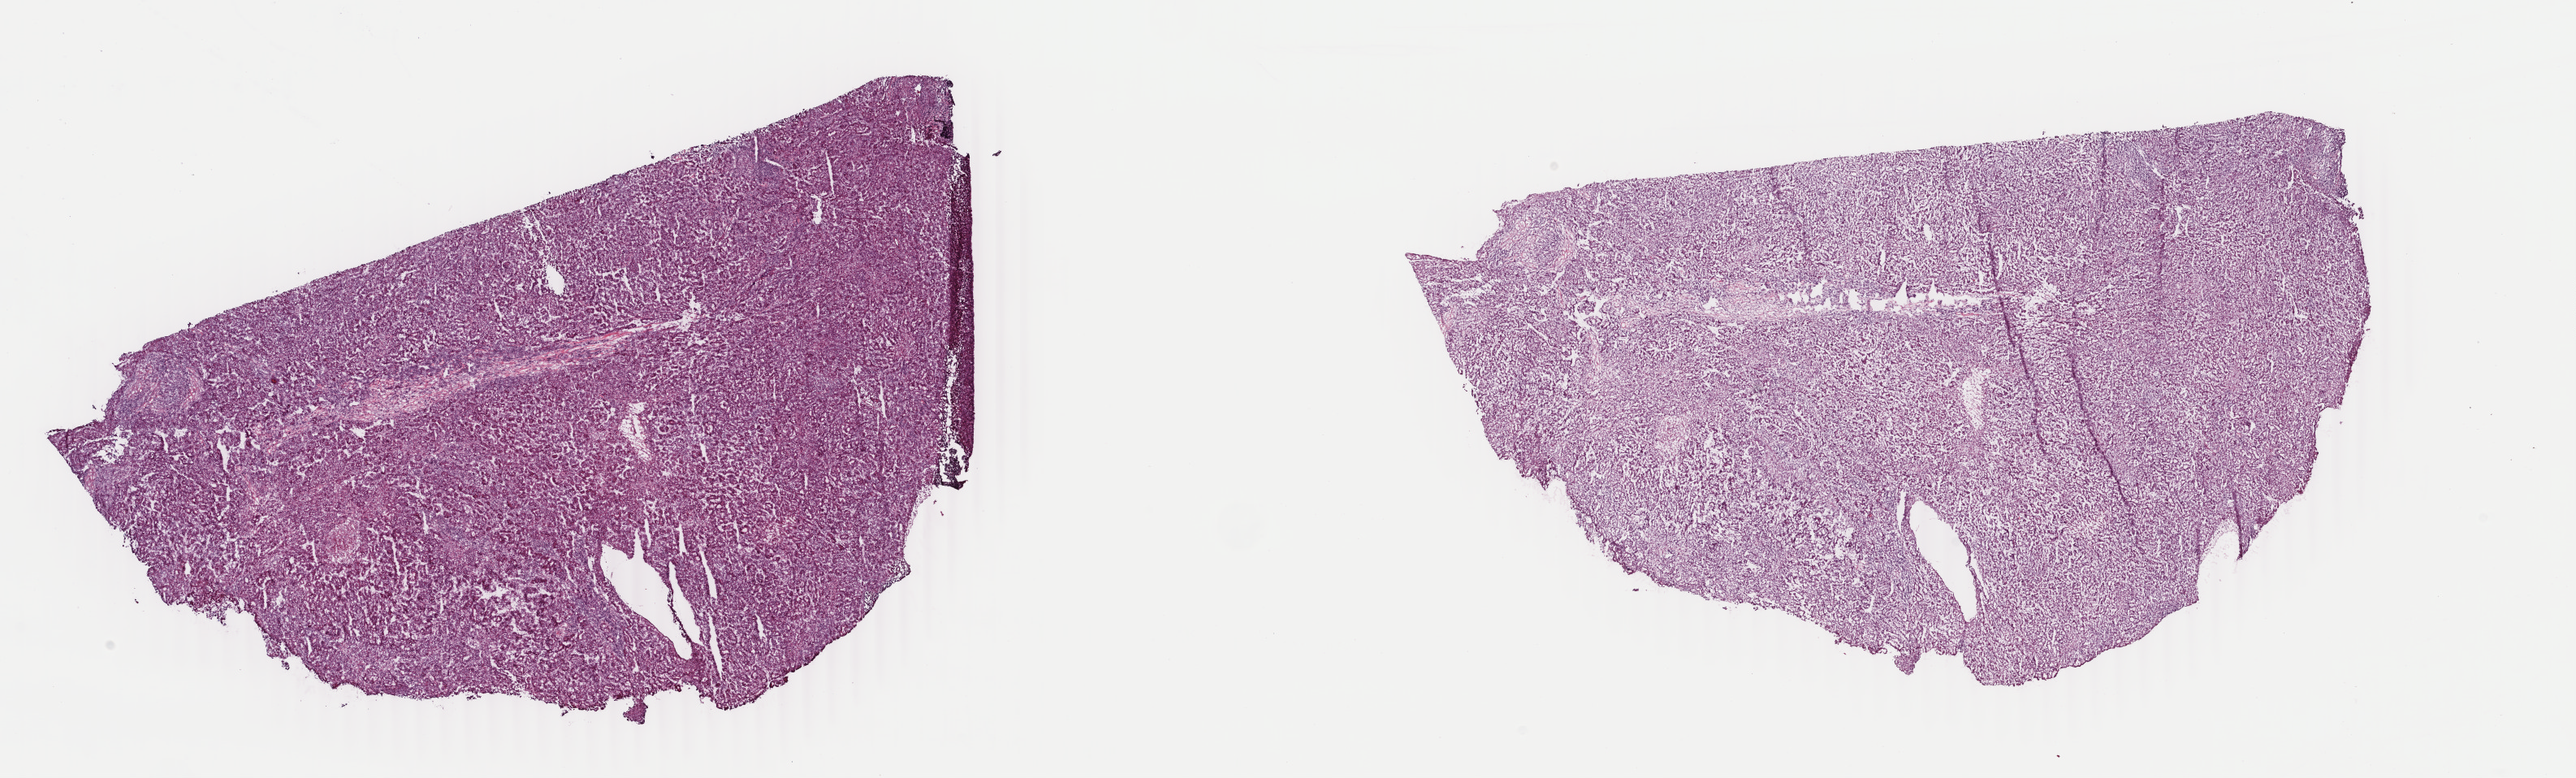
Whole-slide histology image, H&E-stained — low-resolution overview of the scanned area, about 25.2 x 7.6 mm (slide scanned at 40x); frozen section from the top of the tissue portion; sample: primary tumour, liver. Male, age 59 years at initial diagnosis. Histologic grade: G2 (moderately differentiated). Pathologist review of this section (percent, as recorded): tumour cells 90%, tumour nuclei 90%, normal cells 0%, stromal cells 5%, necrosis 5%. Inflammatory infiltration, as recorded: lymphocyte infiltration 0%, monocyte infiltration 0%, neutrophil infiltration 0%.
* AJCC pathologic stage: I (7th edition)
* TNM: T1 NX M0
* histologic diagnosis: Hepatocellular carcinoma, NOS